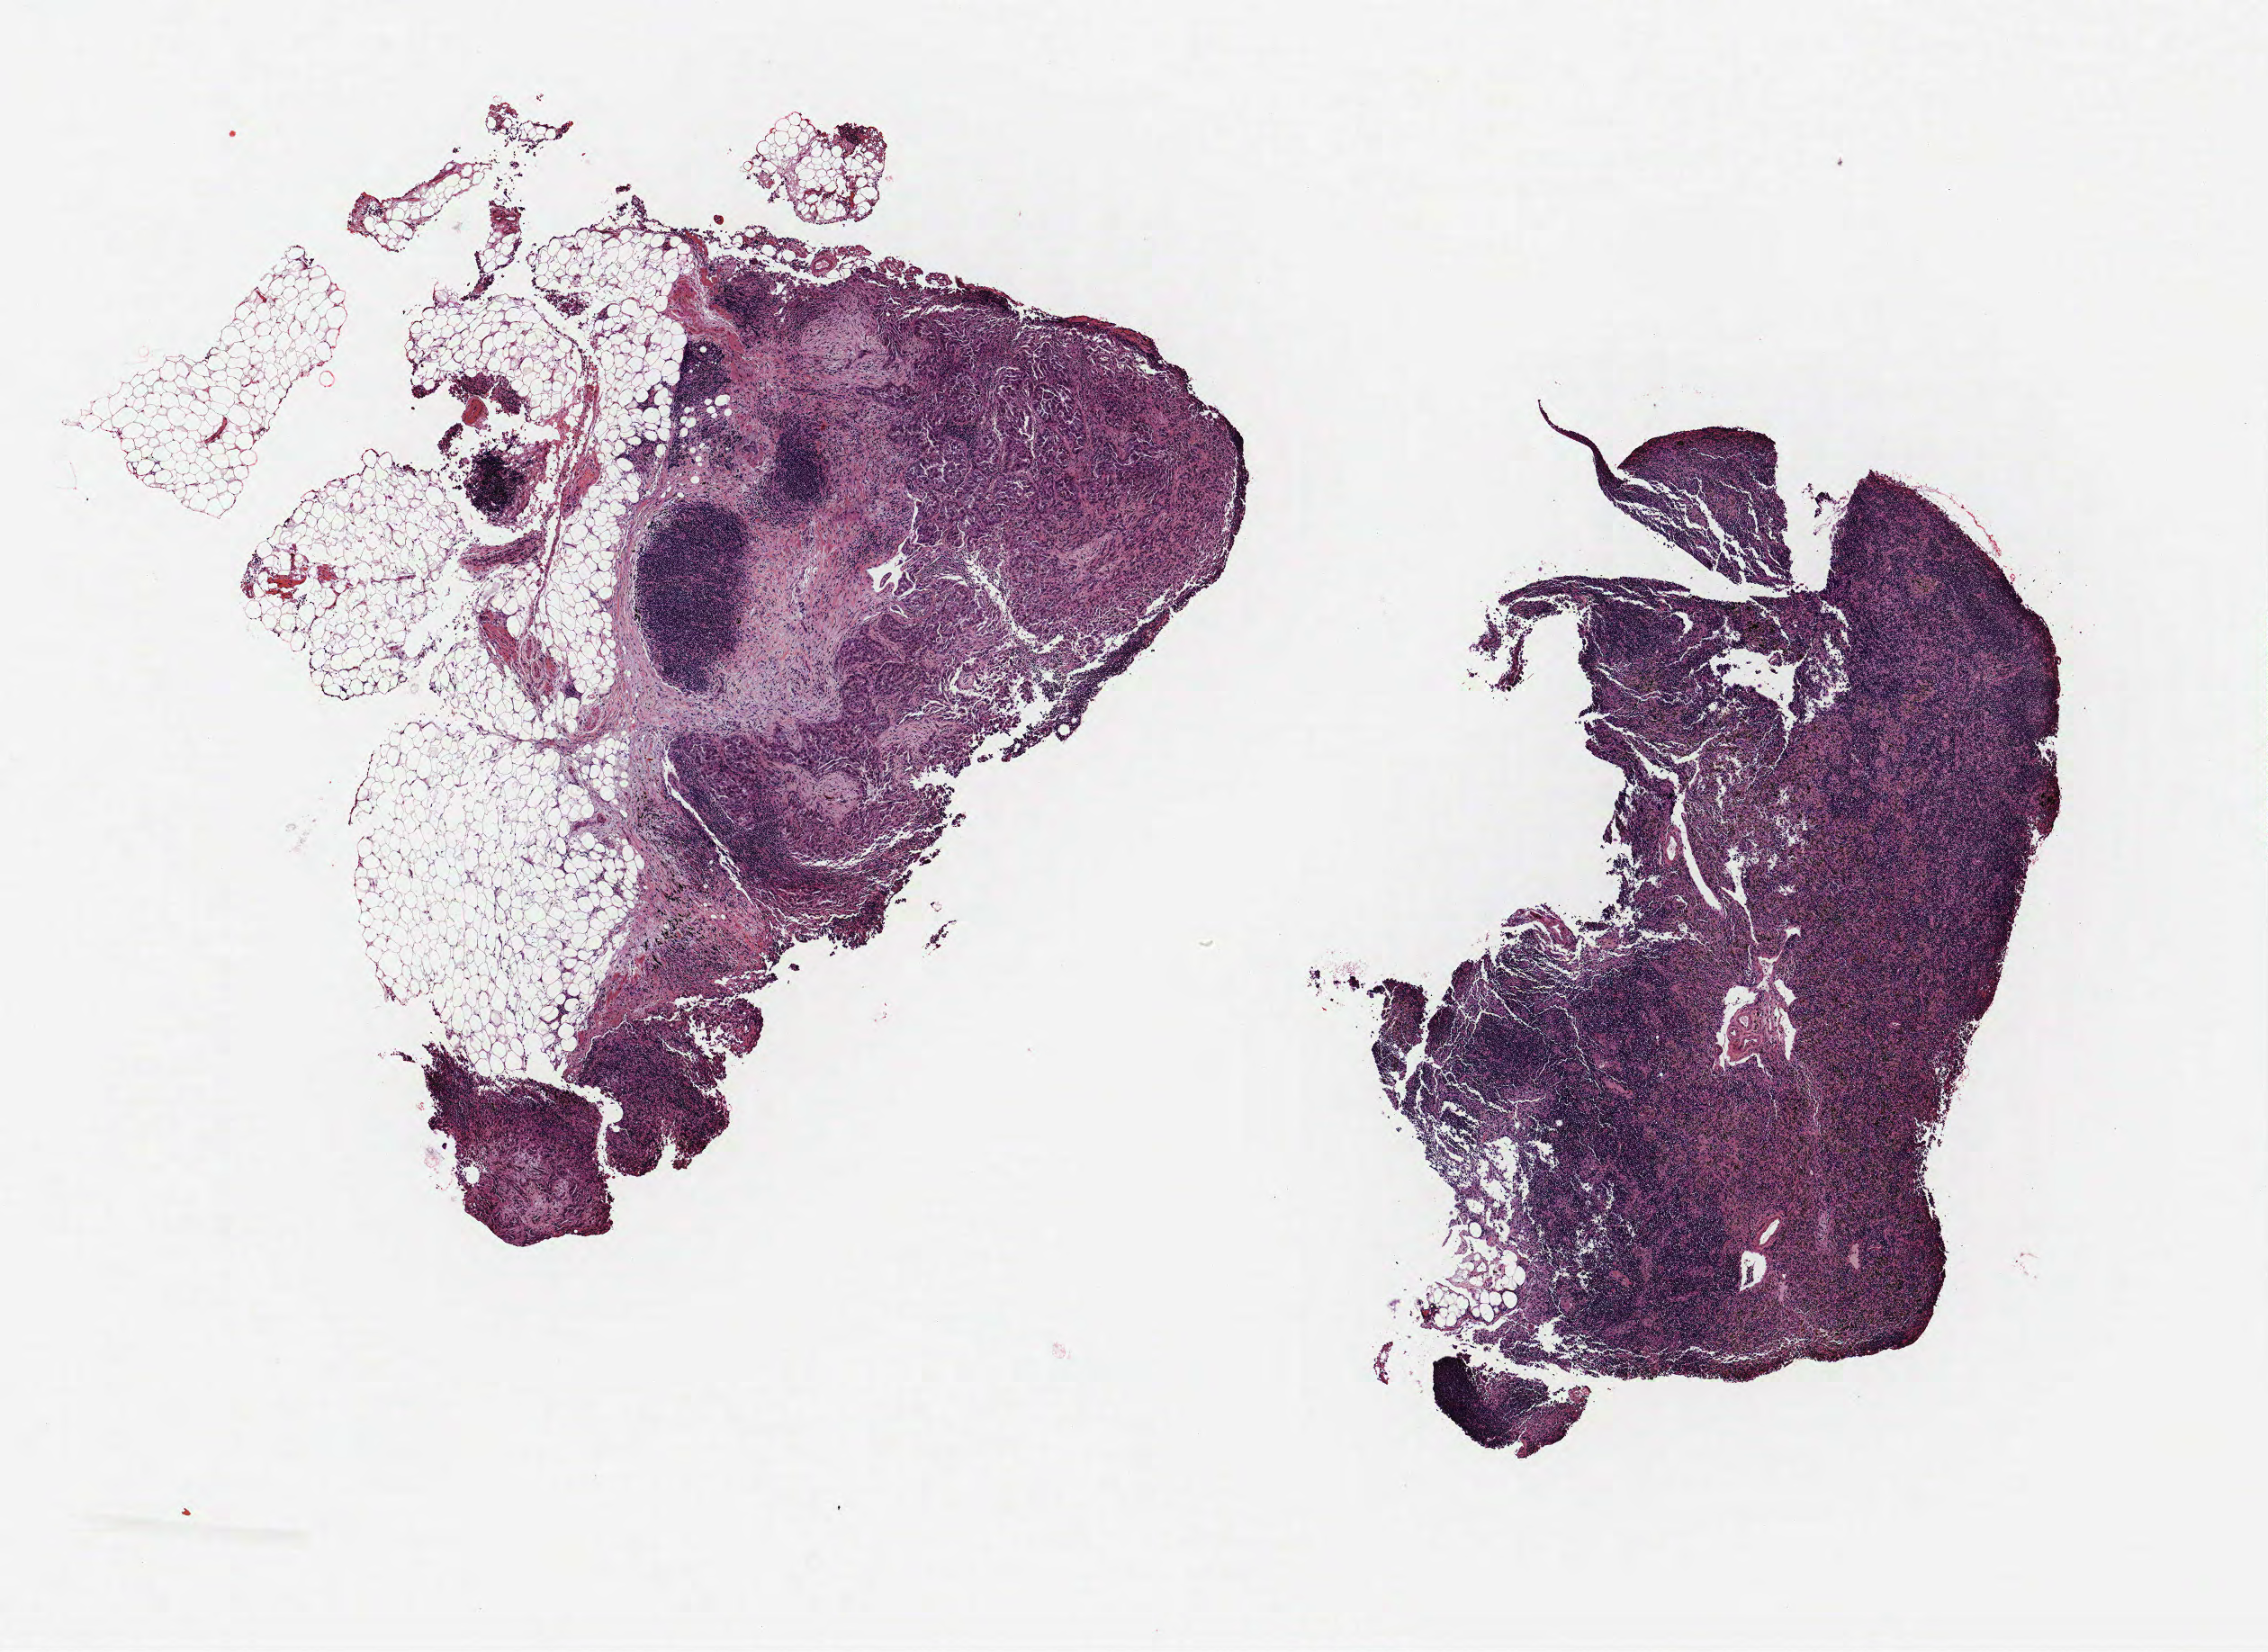
Whole-slide histology image, H&E, low-resolution overview of the scanned area, about 10.1 x 7.3 mm (slide scanned at 40x), formalin-fixed paraffin-embedded (FFPE) section, lung. Male patient, aged 60 at enrolment. Grade: cannot be assessed (GX).
Primary tumour location (clinical record): right upper lobe, right lower lobe, mediastinum. Participant's lung-cancer diagnosis: Adenocarcinoma, NOS. Stage (AJCC 6th edition): IV.